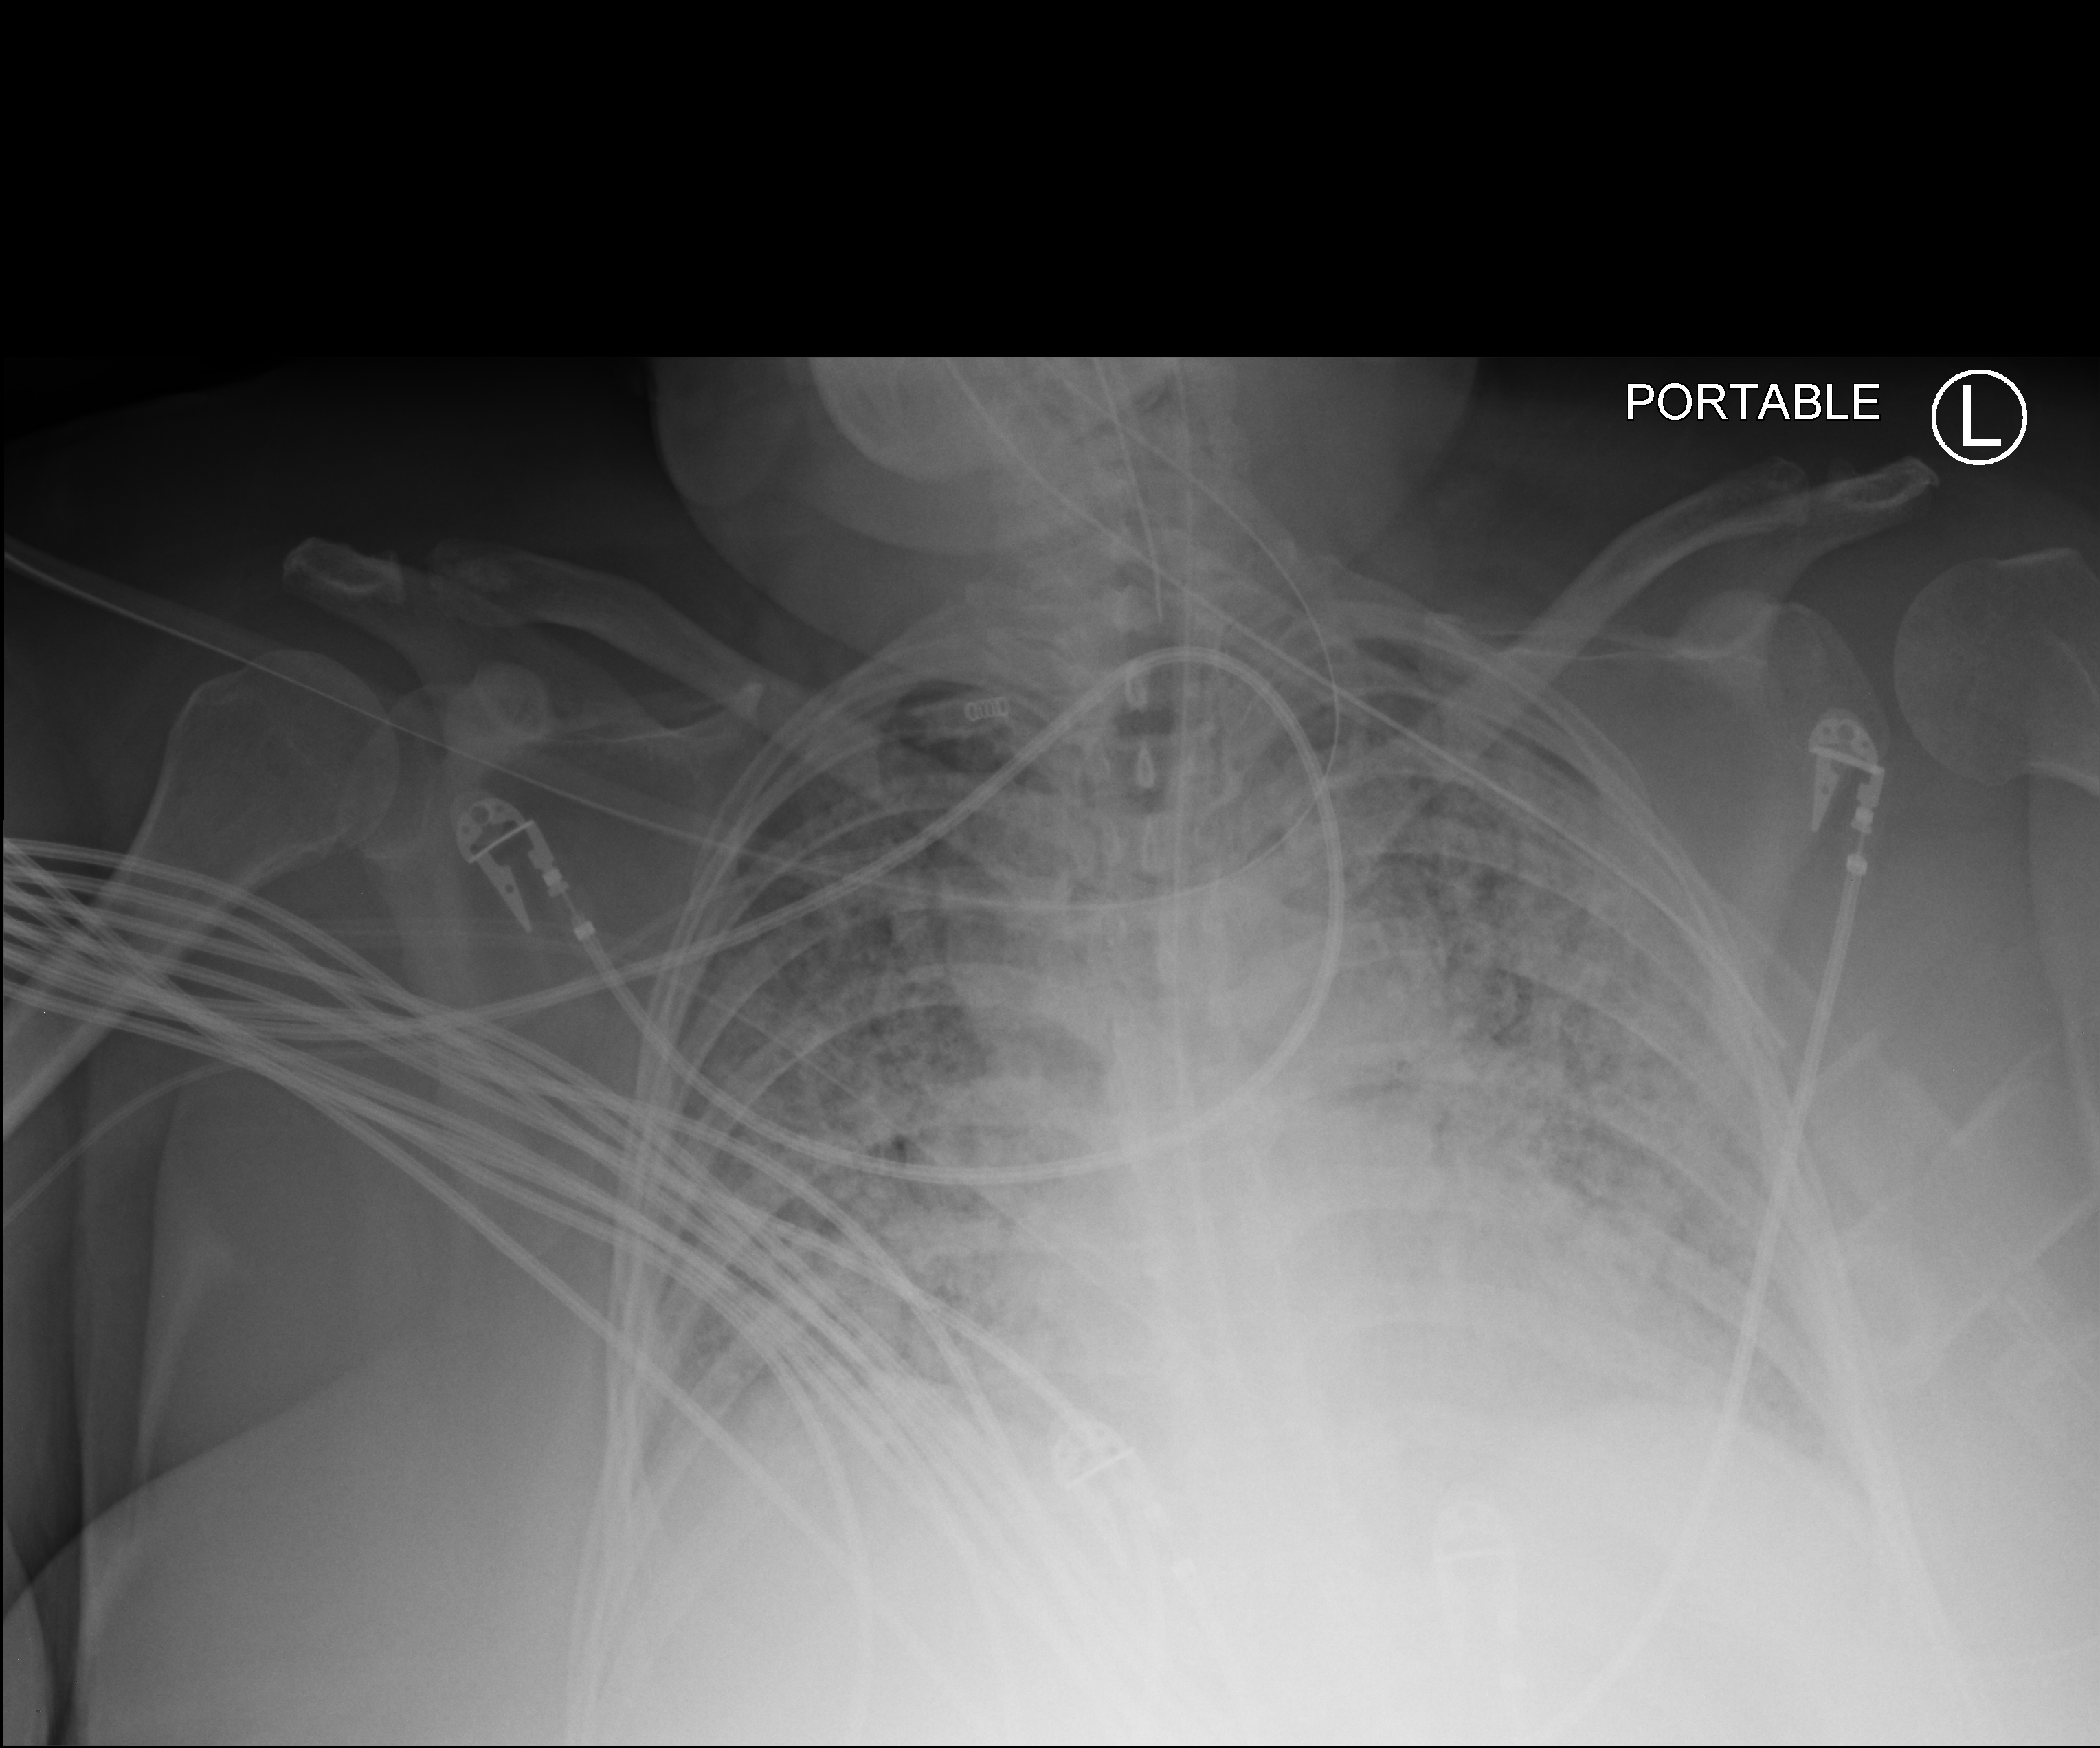
Bedside chest radiograph (computed radiography); anteroposterior (AP) projection. Female patient hospitalised with COVID-19, age 18–59 years.
Admission-level facts for this patient (not findings on this image; timing relative to this image not recorded): chronic kidney disease (admission record): no; length of hospital stay: 95 days; admitted to intensive care during this hospital stay: yes.